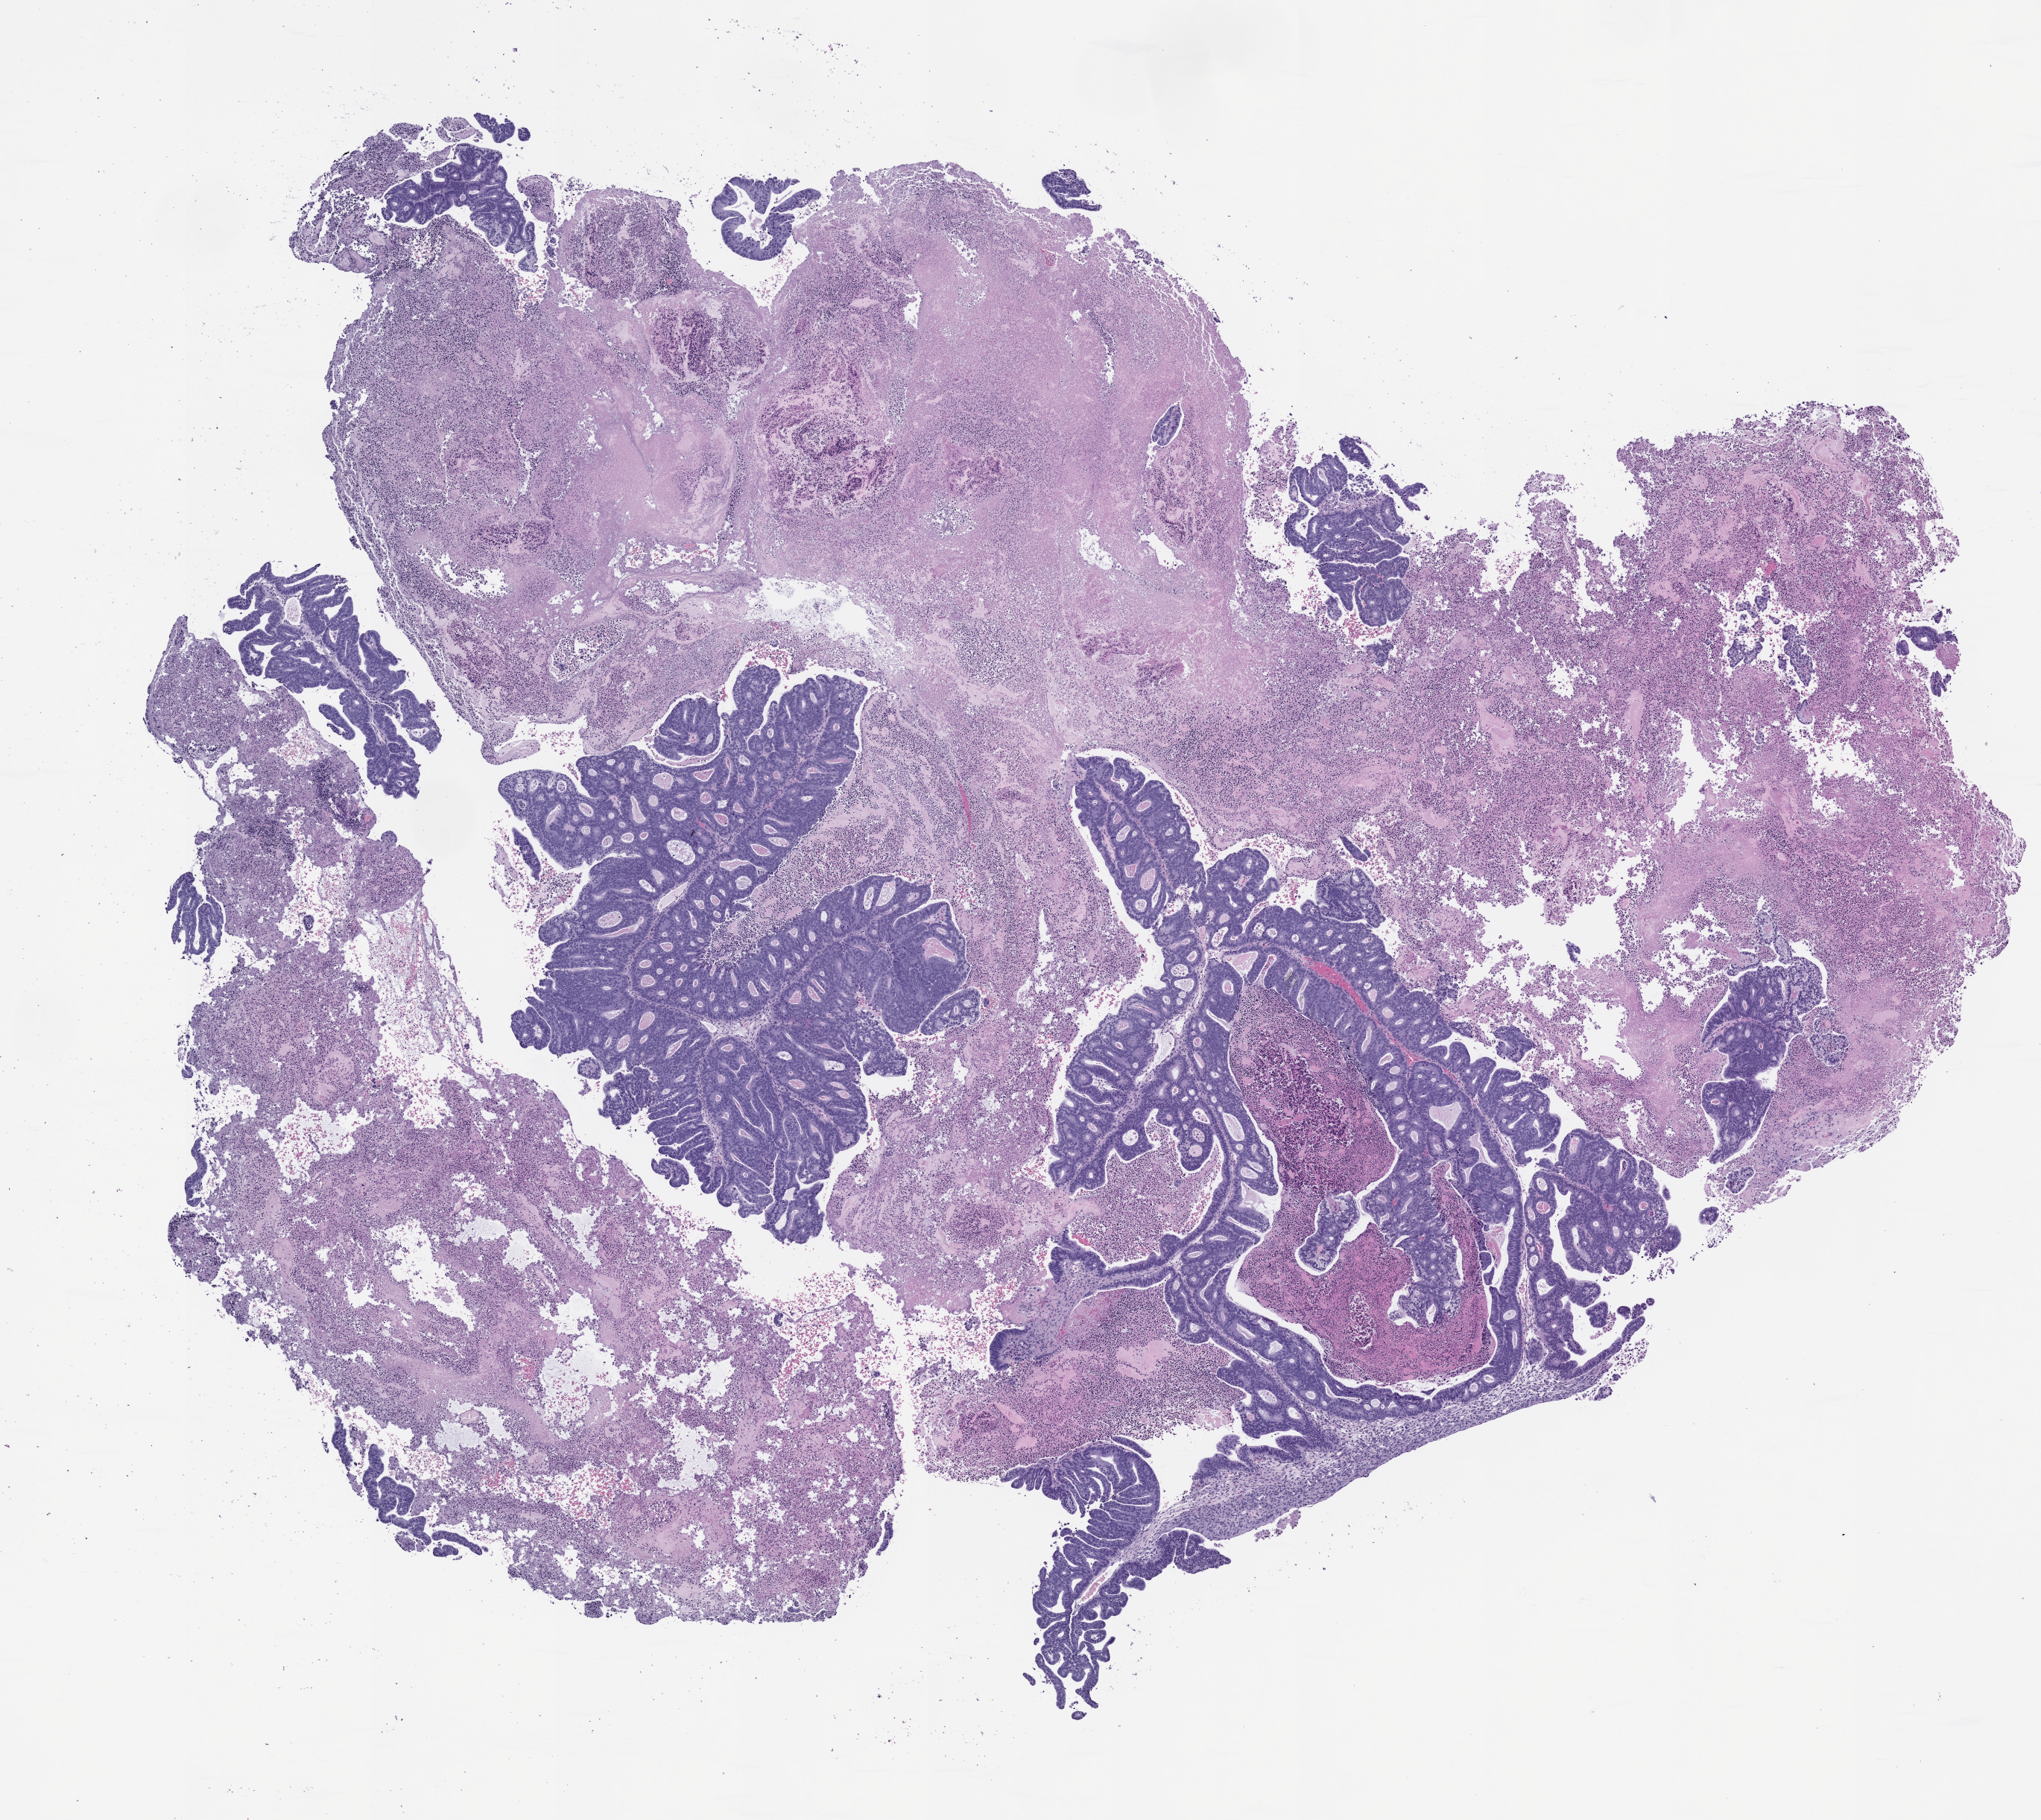
H&E whole-slide image of a patient-derived xenograft (PDX) tumor grown in a mouse, passage 1 — a low-resolution overview of the entire scanned area, about 11.0 x 9.8 mm, formalin-fixed paraffin-embedded section, tumor site category: colon.
Originating patient diagnosis: Colon Adenocarcinoma.